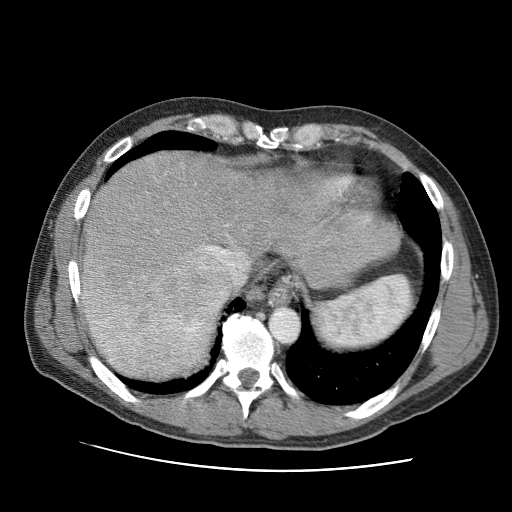
Contrast-enhanced abdominal CT (liver protocol), one axial slice; position 79 of 95 along the scan axis; 120 kVp; one of 2 acquisitions stored at this slice position; soft-tissue window (W 400 / L 40 HU); 2.5 mm slice thickness; 512 × 512 image matrix, field of view 360 × 360 mm. From the clinical record (not read from this slice): diagnosis: hepatocellular carcinoma (patient treated with transarterial chemoembolisation; whether this scan precedes or follows treatment is not stated here); TNM stage (as recorded): Stage-IVA; Child-Pugh class: A; tumour nodularity: multinodular.
Outlined on this slice (semi-automatically segmented with operator editing):
- liver parenchyma outside the tumour (the mass and vessels are separate outlines, so this box may not span the whole liver): bounding box (x1, y1, x2, y2) in pixels: (80, 150, 400, 317)
- mass: (84, 260, 223, 380)
- liver vessels: (156, 224, 249, 295)